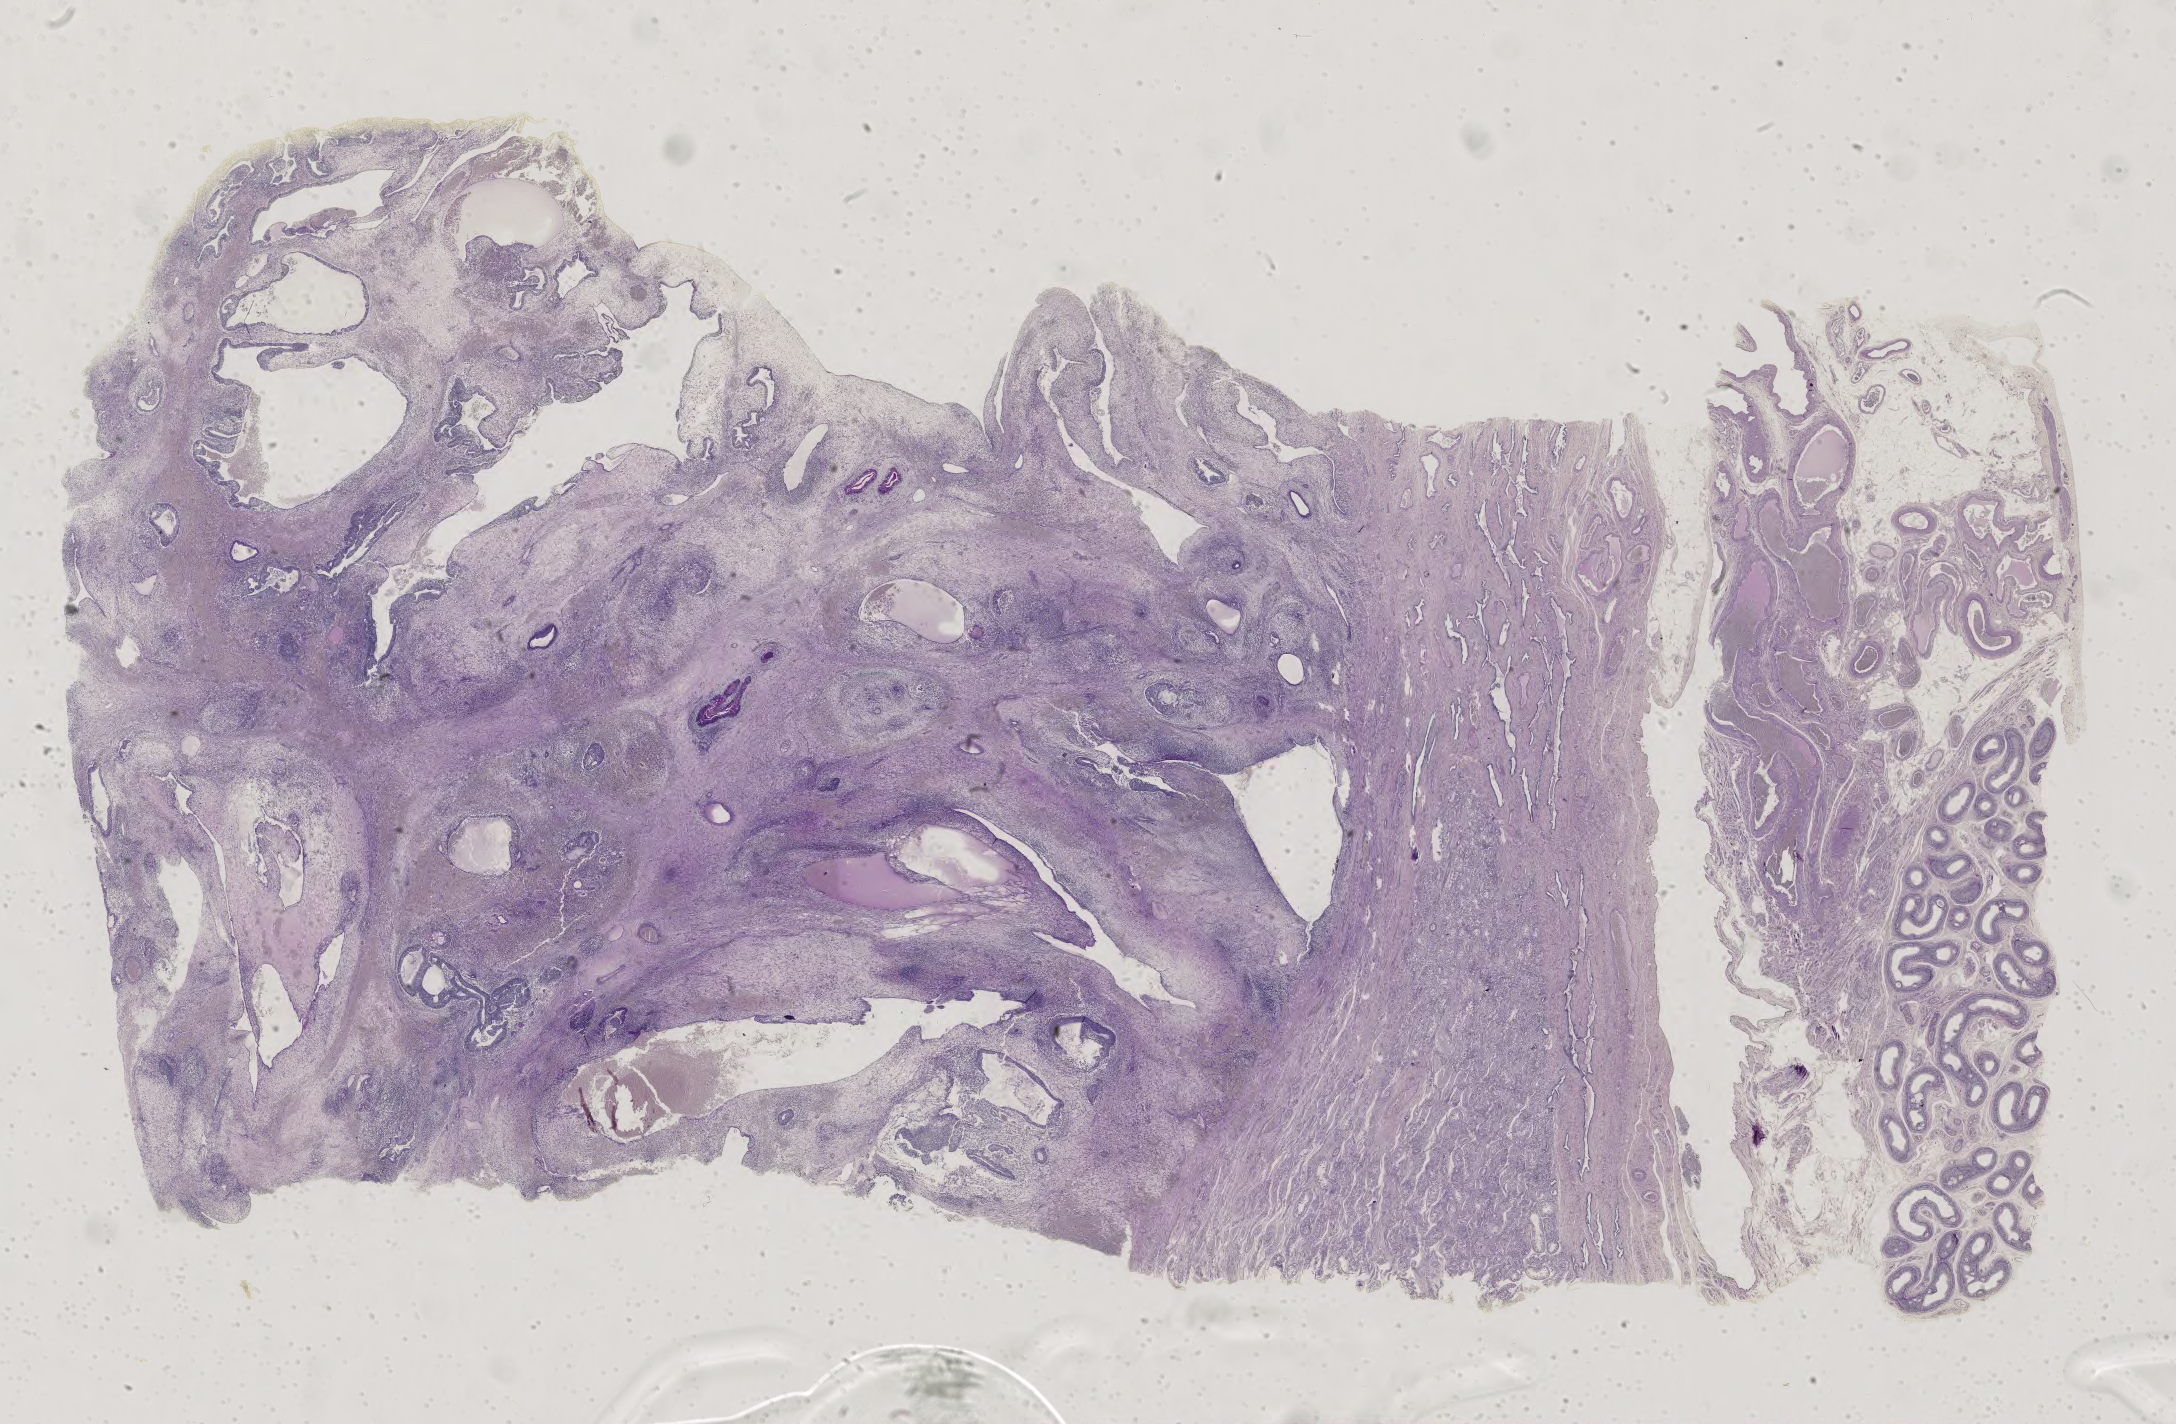
Whole-slide histology image, Hematoxylin and eosin (H&E) stained — low-resolution overview of the scanned area, about 31.7 x 20.8 mm, FFPE section, sample: primary tumour, testis. Patient: male, age at initial diagnosis 28 years.
* AJCC pathologic stage: IS
* diagnosis: Teratoma, benign